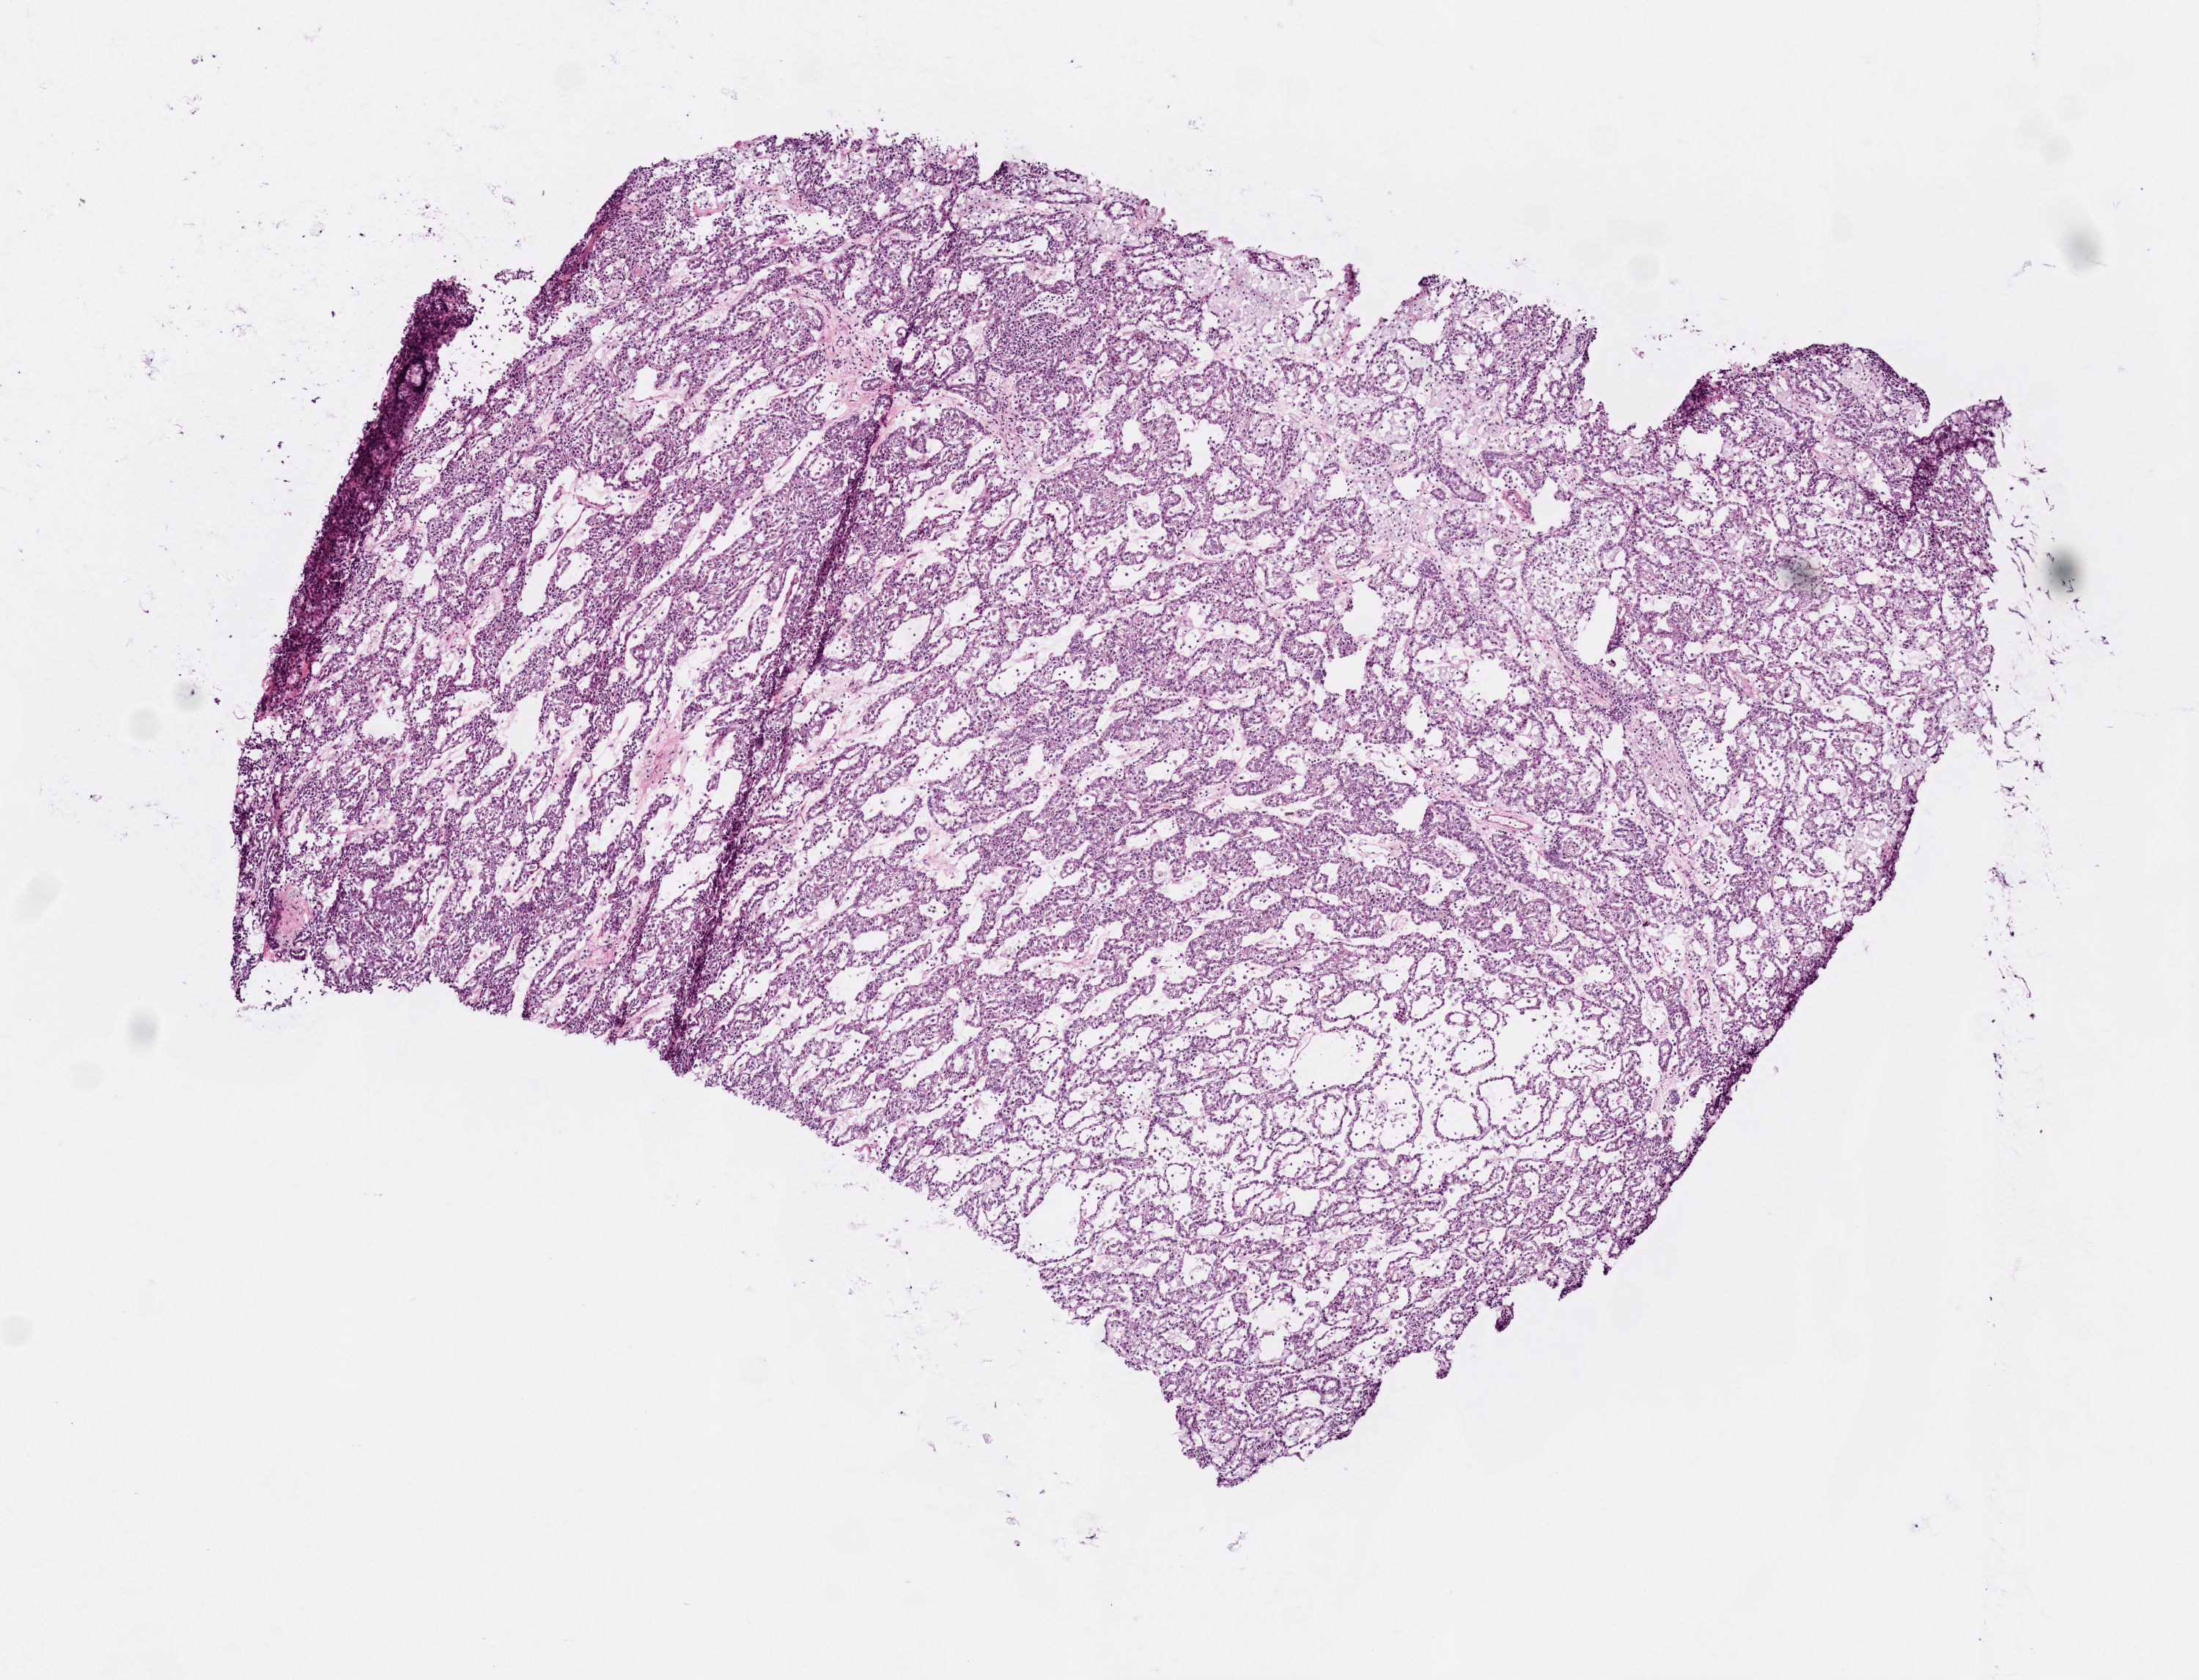
H&E whole-slide image, shown as a low-resolution overview of the whole scanned area (about 6.0 x 4.6 mm); frozen section from the top of the tissue portion; primary tumour sample from the kidney. Male, age 64 years at initial diagnosis.
Pathologic diagnosis: Papillary adenocarcinoma, NOS.